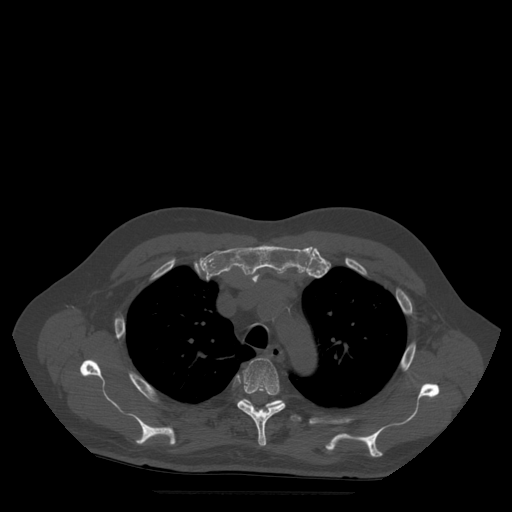
CT including the spine, one axial slice; position 388 of 522 along the scan axis; bone window (W 1800 / L 400 HU); 1.25 mm slice thickness; 512 × 512 image matrix, field of view 420 × 420 mm. Patient age 72 years. Case-level facts recorded for this patient, not image findings: primary cancer: prostate.
Structures marked on this image (semi-automatic segmentation, software-assisted and operator-edited):
- T4 vertebra: bounding box [x1, y1, x2, y2] px = [238, 358, 286, 447]
- T5 vertebra: [239, 400, 316, 424]